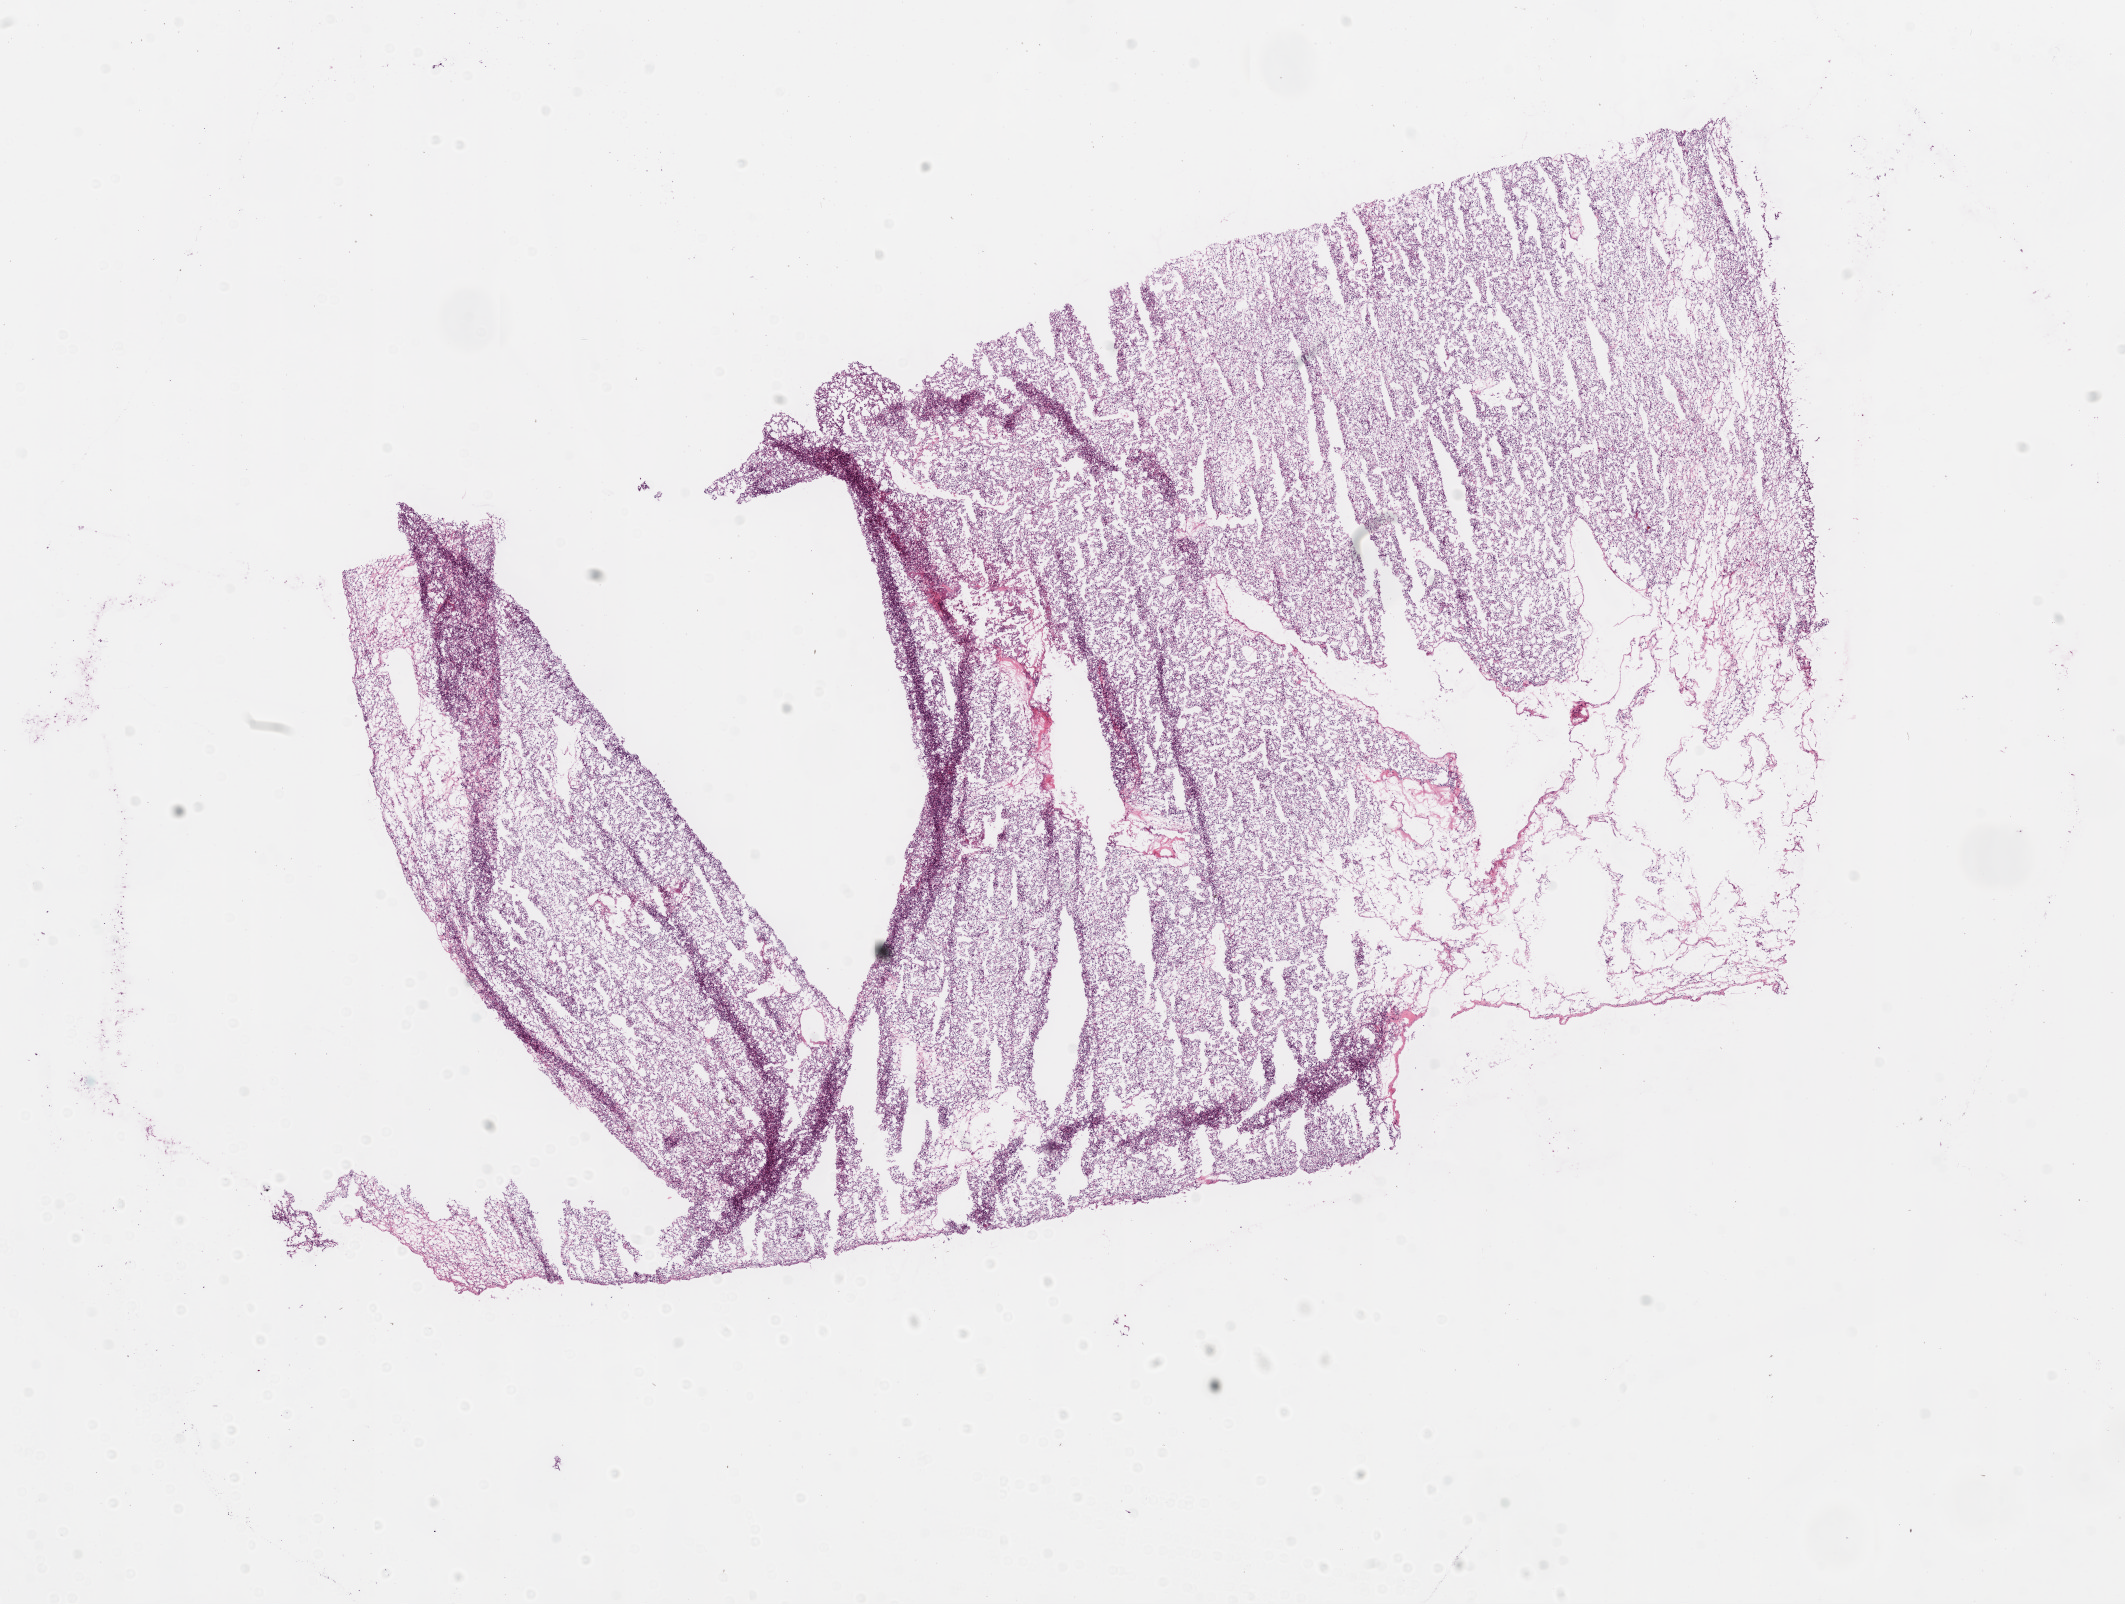
H&E-stained whole-slide image, a low-resolution overview of the entire scanned area, about 17.1 x 12.9 mm, frozen section, sample: primary tumour, kidney. Patient: male, age at initial diagnosis 62 years. Slide review estimates, as recorded: tumour cells 95%, tumour nuclei 75%.
Diagnosis: Clear cell adenocarcinoma, NOS.